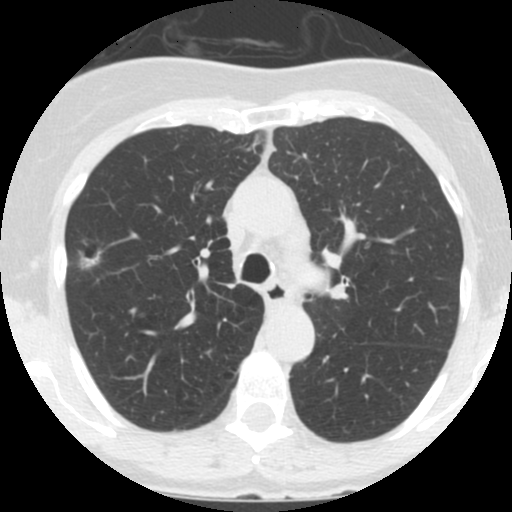
Chest CT (low-dose screening protocol), one axial image; third annual screen; lung window (W 1500 / L -600 HU); 2.5 mm slice thickness; standard (soft-tissue) reconstruction kernel (STANDARD); slice 48 of 146 in the series. Female, age 60 years at enrolment. Current smoker at enrolment.
Expert reader's lesion annotation, bounding box <63,232,112,284> (left, top, right, bottom; pixels). Screening reader's record for this exam (one nodule recorded; not confirmed to be the boxed lesion): non-calcified nodule or mass ≥4 mm, right upper lobe, 12 × 12 mm, smooth margins, ground glass attenuation, pre-existing on the prior screen: yes; interval growth: yes. Official screen result: positive, other. Lung cancer was diagnosed 56 days after this screen: bronchiolo-alveolar adenocarcinoma, NOS, right upper lobe, well differentiated (G1), stage IA (AJCC 6th edition), 11 mm at pathology.